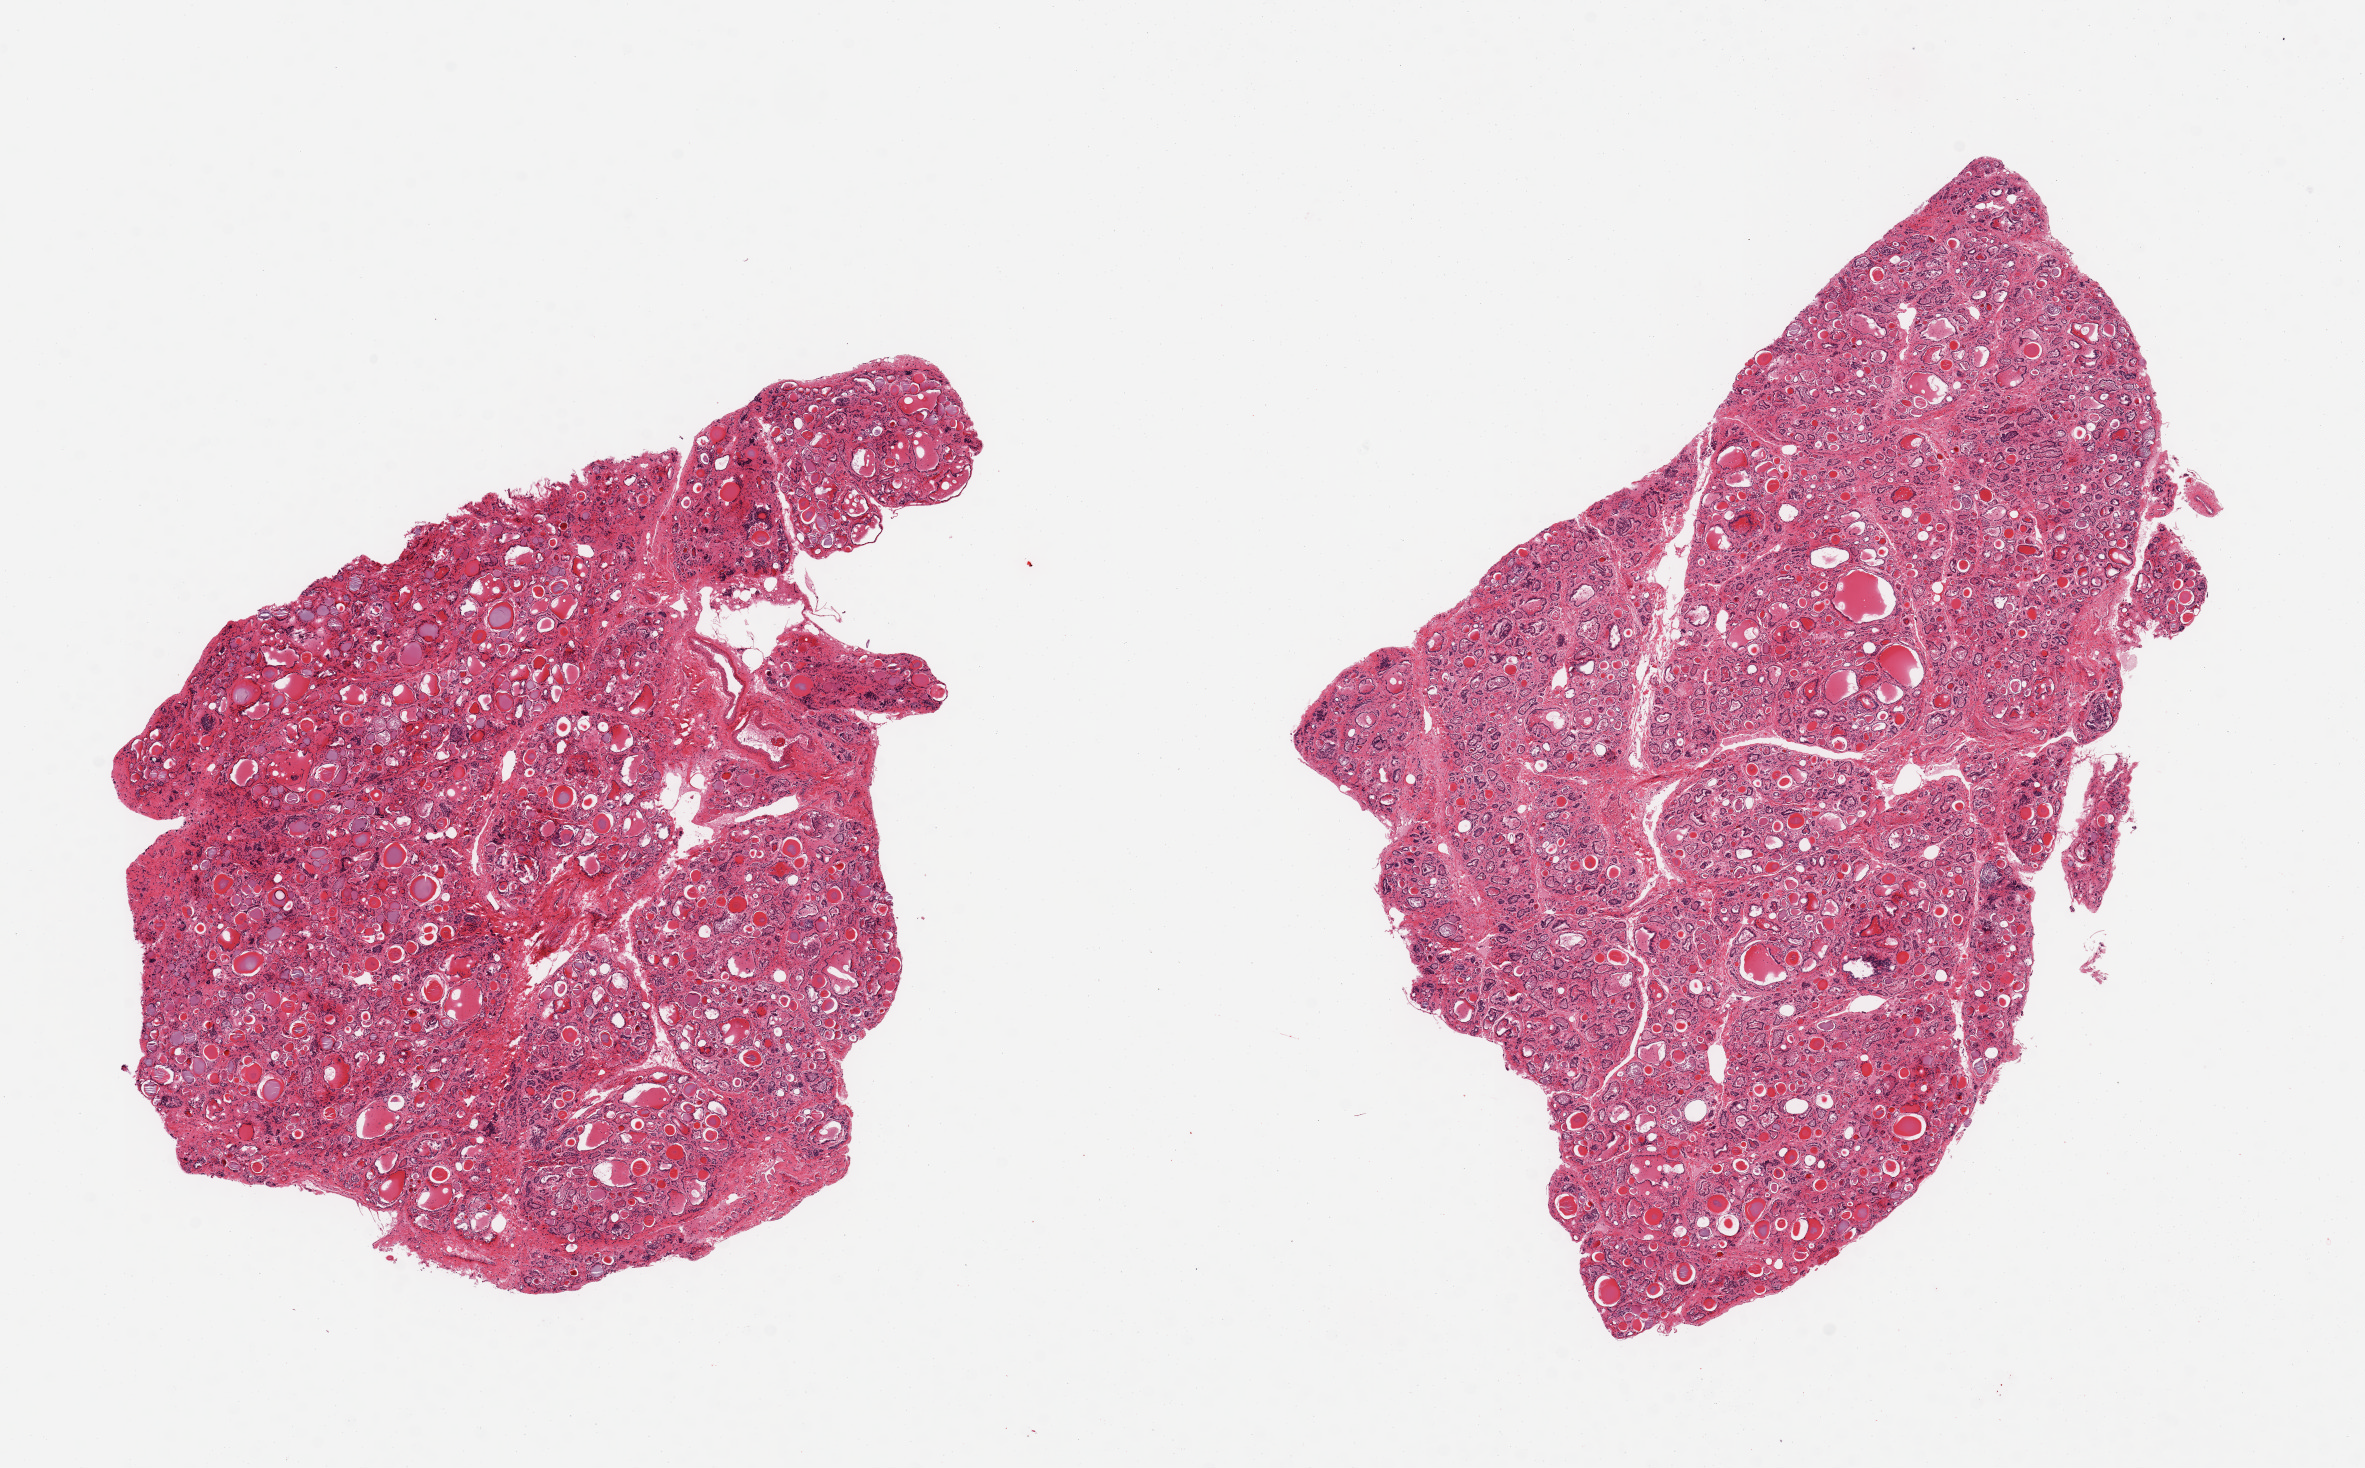
H&E whole-slide image, brightfield — whole scanned area (about 18.7 x 11.6 mm, from a 20x scan) shown as a low-resolution overview, PAXgene-fixed paraffin-embedded (PFPE) section, section of thyroid (target tissue), donor tissue sample. Donor: male.
Review note (as recorded): 2 pieces, diffuse micronodular goiter, regressive changes.